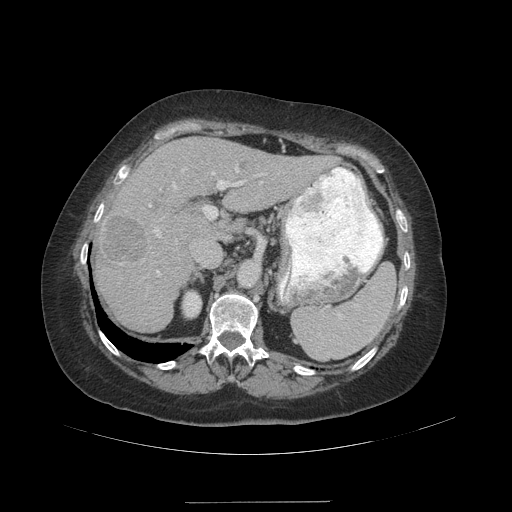
Contrast-enhanced abdominal CT (liver protocol), one axial slice; slice 67 of 99 in the series (ordered by position); 140 kVp; soft-tissue window (W 400 / L 40 HU); 2.5 mm slice thickness; 512 × 512 image matrix, field of view 440 × 440 mm. Case-level facts recorded for this patient, not image findings: diagnosis: hepatocellular carcinoma (patient treated with transarterial chemoembolisation; whether this scan precedes or follows treatment is not stated here); TNM stage (as recorded): Stage-IVA; Child-Pugh class: A.
Outlined on this slice (semi-automatic segmentation, software-assisted and operator-edited):
- liver parenchyma outside the tumour (the mass and vessels are separate outlines, so this box may not span the whole liver): bounding box <94,138,327,332> (left, top, right, bottom; pixels)
- mass: <98,213,149,263>
- liver vessels: <149,167,263,276>